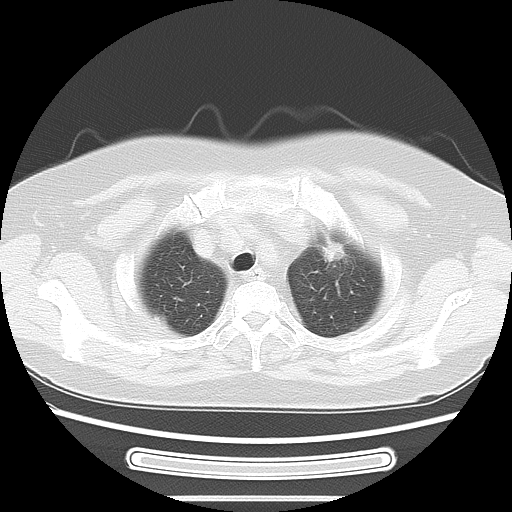
Chest CT, one axial slice; reconstruction kernel LUNG; 120 kVp; lung window (W 1500 / L -600 HU); 5 mm slice thickness; 512 × 512 image matrix. Female patient, age 70 years. Case-level facts recorded for this patient, not image findings: clinical TNM (as recorded): T1c N0 M0; histopathological grade: G2-3.
Structures marked on this image (rectangle marked by the reading radiologist):
- lung tumour (recorded histology: adenocarcinoma): bounding box <318,232,346,269> (left, top, right, bottom; pixels)